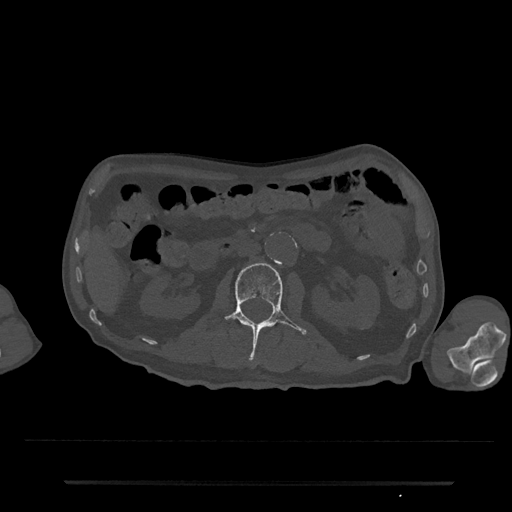
CT including the spine, one axial slice; position 63 of 797 along the scan axis; reconstruction kernel Br40s/3; 120 kVp; bone window (W 1800 / L 400 HU); 512 × 512 image matrix, field of view 427 × 427 mm. Male patient, age 74 years. From the clinical record (not read from this slice): primary cancer: prostate.
Outlined on this slice (semi-automatically segmented with operator editing):
- L2 vertebra: box from (x=223, y=263) to (x=307, y=358) px